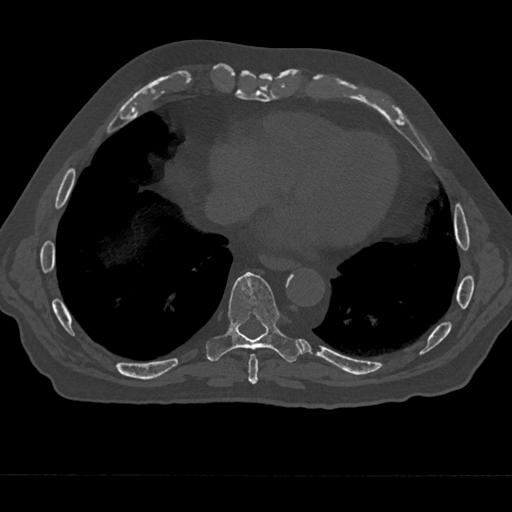
CT including the spine, one axial slice; position 270 of 797 along the scan axis; bone window (W 1800 / L 400 HU); 512 × 512 image matrix, field of view 377 × 377 mm. Male patient, age 75 years. From the clinical record (not read from this slice): primary cancer: renal.
Annotated regions visible in this slice (semi-automatically segmented with operator editing):
- T8 vertebra: box from (x=248, y=354) to (x=258, y=385) px
- T9 vertebra: (x=206, y=272)–(x=302, y=362)